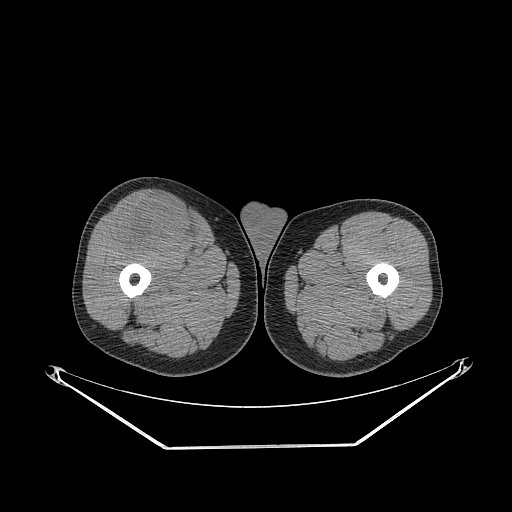
CT of an extremity soft-tissue mass (from a PET/CT study), one axial slice; slice 275 of 311 in the series (ordered by position); reconstruction kernel STANDARD; 140 kVp; soft-tissue window (W 400 / L 40 HU); 3.75 mm slice thickness; 512 × 512 image matrix, field of view 500 × 500 mm. Male patient. From the clinical record (not read from this slice): histological type: pleiomorphic leiomyosarcoma; grade: intermediate; site of the primary tumour: right thigh.
Annotated regions visible in this slice (expert contour drawn on MRI and transferred to this co-registered scan by the dataset authors):
- gross tumour volume including surrounding oedema: bounding box <114,196,197,257> (left, top, right, bottom; pixels)
- gross tumour volume (mass): <114,196,197,257>